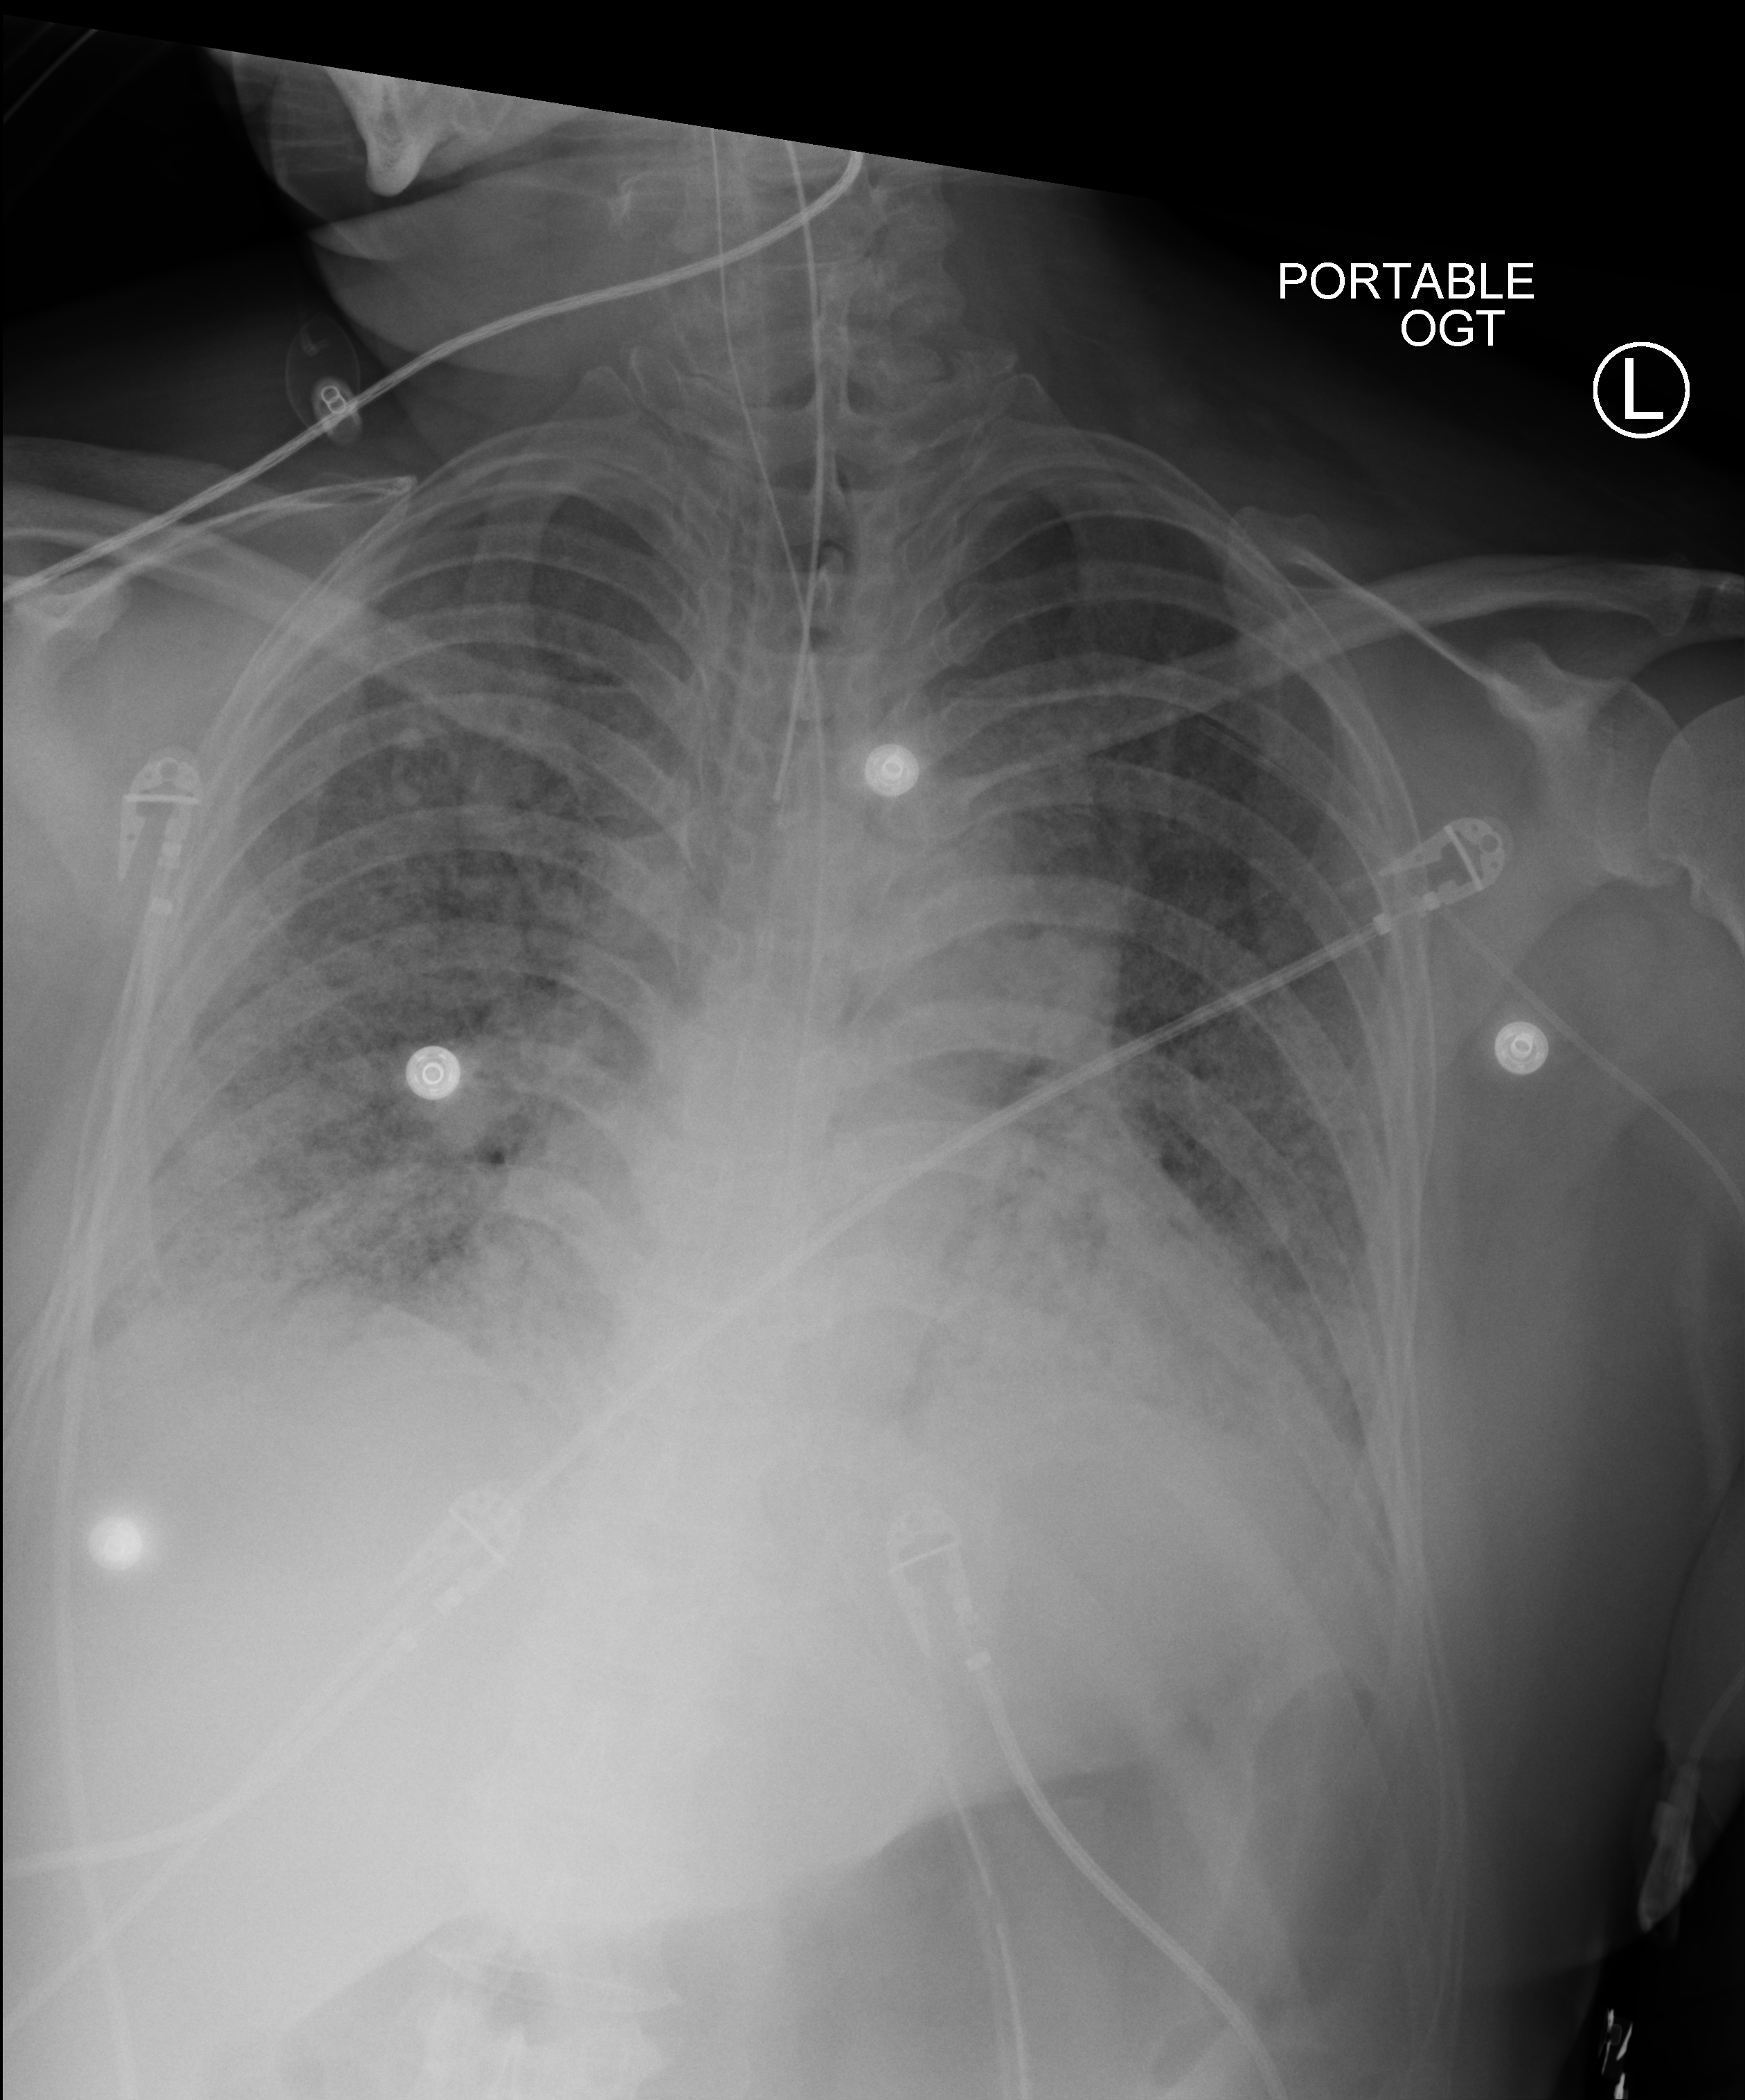
Portable chest radiograph, anteroposterior (AP) projection. Adult patient hospitalised with COVID-19, age 18–59 years.
Admission-level facts for this patient (not findings on this image; timing relative to this image not recorded): admitted to intensive care during this hospital stay: yes.